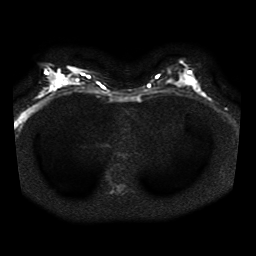
Breast MRI, one axial slice. Slice 18 of 41 in the series (ordered by position). Diffusion-weighted series; image 2 of 4 stored at this slice position (different b-values; order by instance number). 1.5 T. 5 mm slice thickness. 256 × 256 image matrix, field of view 320 × 320 mm. Female patient.
Annotated regions visible in this slice (expert manual segmentation):
- tumour on diffusion-weighted imaging: bounding box [x1, y1, x2, y2] px = [184, 76, 194, 88]